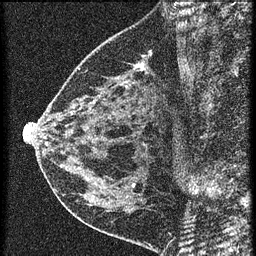
Breast MRI (dynamic contrast-enhanced), one sagittal slice; slice 25 of 60 in the series (ordered by position); 3 images stored at this slice position (order not interpretable as contrast timing); 1.5 T; TE 4.2 ms, TR 20.4 ms; 1.5 mm slice thickness; 256 × 256 image matrix. Patient: female, 46 years. Case-level facts recorded for this patient, not image findings: setting: breast cancer imaged before/during neoadjuvant chemotherapy; receptor status: HR-positive, HER2-negative.
Outlined on this slice (semi-automatically segmented with operator editing):
- analysis volume of interest (the breast-tissue region the enhancement analysis was run in; not a lesion): bounding box <58,36,169,155> (left, top, right, bottom; pixels)
- tumour enhancement mask (voxels above the 90 % enhancement threshold inside the analysis volume of interest): <138,64,145,69>